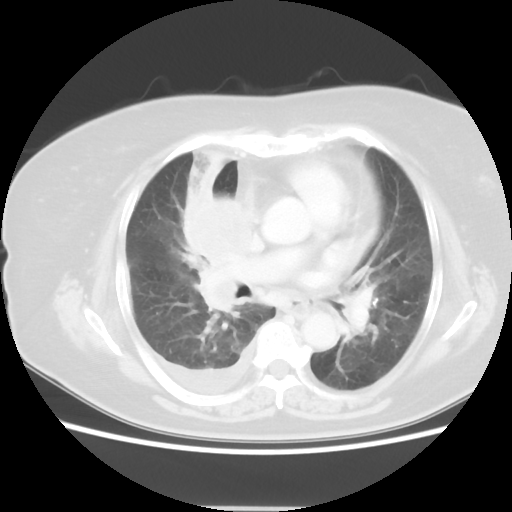
Chest CT, one axial slice; slice 27 of 48 in the series (ordered by position); reconstruction kernel STANDARD; lung window (W 1500 / L -600 HU); 5 mm slice thickness; 512 × 512 image matrix, field of view 360 × 360 mm. Patient: female, 73 years. Case-level facts recorded for this patient, not image findings: clinical TNM (as recorded): T3 N3 M1b; histopathological grade: G3.
Annotated regions visible in this slice (bounding box drawn by a radiologist):
- lung tumour (recorded histology: small cell carcinoma): bounding box [x1, y1, x2, y2] px = [183, 145, 251, 320]